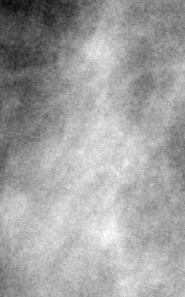
Region of interest cut from a scanned film mammogram (one marked finding), right breast, MLO view.
- Finding: calcifications, morphology punctate / round and regular, distribution regional; BI-RADS assessment category 2; subtlety rating 3 on a 1 (subtle) to 5 (obvious) scale; benign without callback (not worked up further).